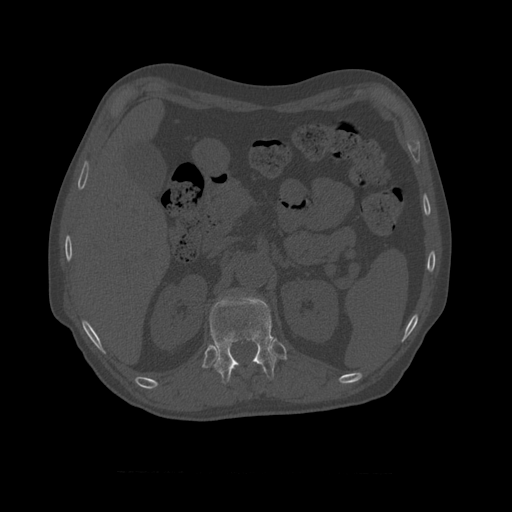
CT including the spine, one axial slice; position 380 of 450 along the scan axis; reconstruction kernel STANDARD; 120 kVp; bone window (W 1800 / L 400 HU); 1.25 mm slice thickness; 512 × 512 image matrix, field of view 405 × 405 mm. Patient age 75 years. Case-level facts recorded for this patient, not image findings: primary cancer: prostate.
Structures marked on this image (semi-automatic segmentation, software-assisted and operator-edited):
- T11 vertebra: box from (x=209, y=294) to (x=278, y=385) px